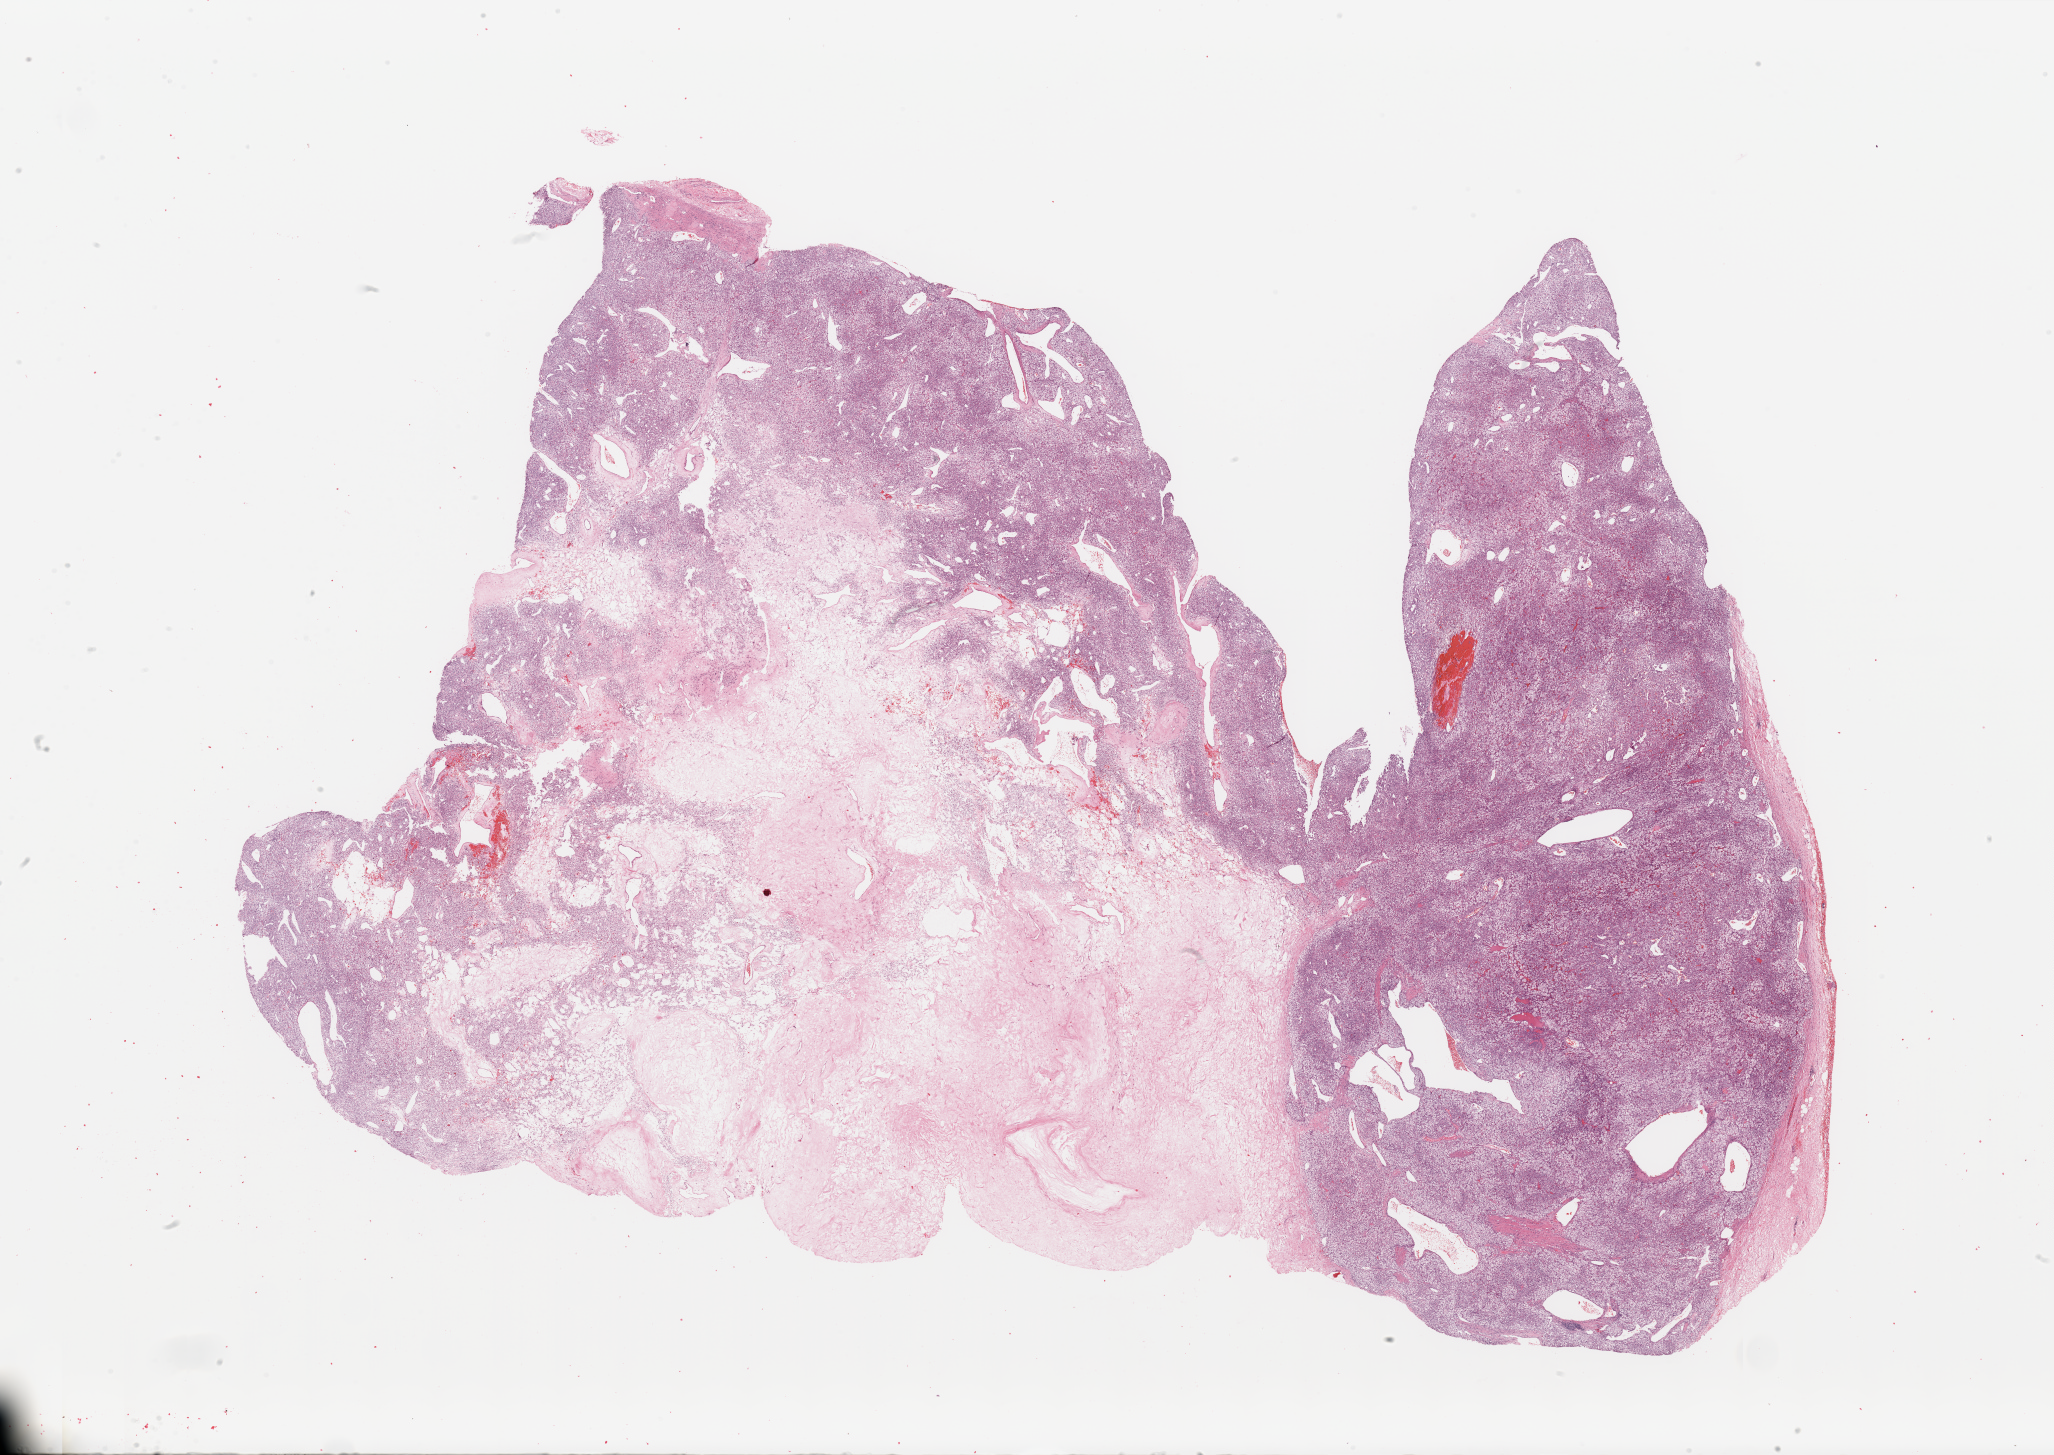
Hematoxylin and eosin (H&E) stained whole-slide image — whole scanned area (about 32.5 x 23.0 mm) shown as a low-resolution overview. Kidney, tumour tissue. Female, 76 y/o. Histologic grade: G2 (moderately differentiated).
* diagnosis: Renal cell carcinoma, NOS